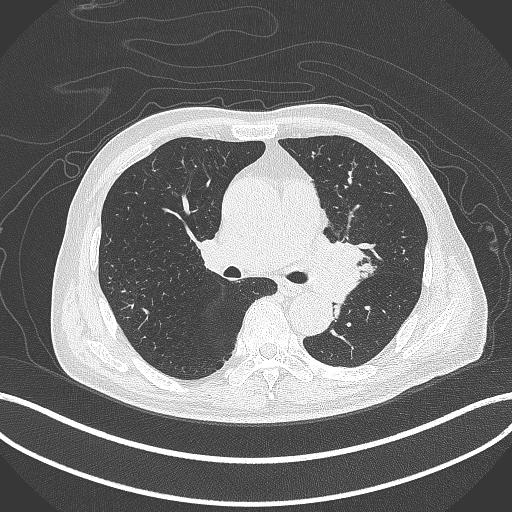
Chest CT, one axial slice. Slice 253 of 417 in the series (ordered by position). Reconstruction kernel B70f. 120 kVp. Lung window (W 1500 / L -600 HU). 1 mm slice thickness. 512 × 512 image matrix, field of view 400 × 400 mm. Male patient, age 77 years. From the clinical record (not read from this slice): clinical TNM (as recorded): T3 N1 M0.
Annotated regions visible in this slice (bounding box drawn by a radiologist):
- lung tumour (recorded histology: adenocarcinoma): bounding box [x1, y1, x2, y2] px = [306, 232, 368, 302]